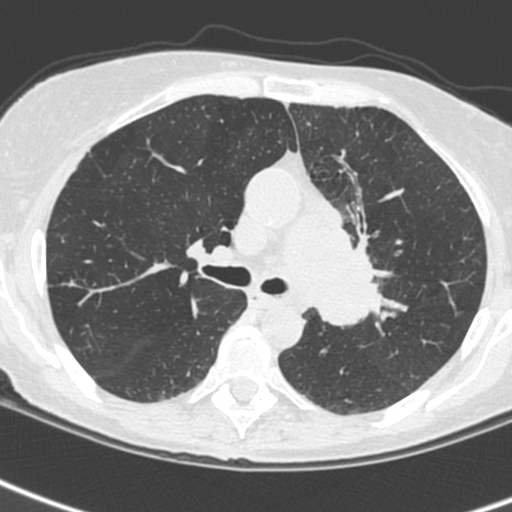
Low-dose screening chest CT, one axial slice; position 157 of 242 along the scan axis; lung window (W 1500 / L -600 HU); 512 × 512 image matrix, field of view 284 × 284 mm.
Annotated regions visible in this slice (expert manual segmentation):
- lesion 3 (tumor, upper lobe of left lung): bounding box [x1, y1, x2, y2] px = [314, 204, 380, 327]